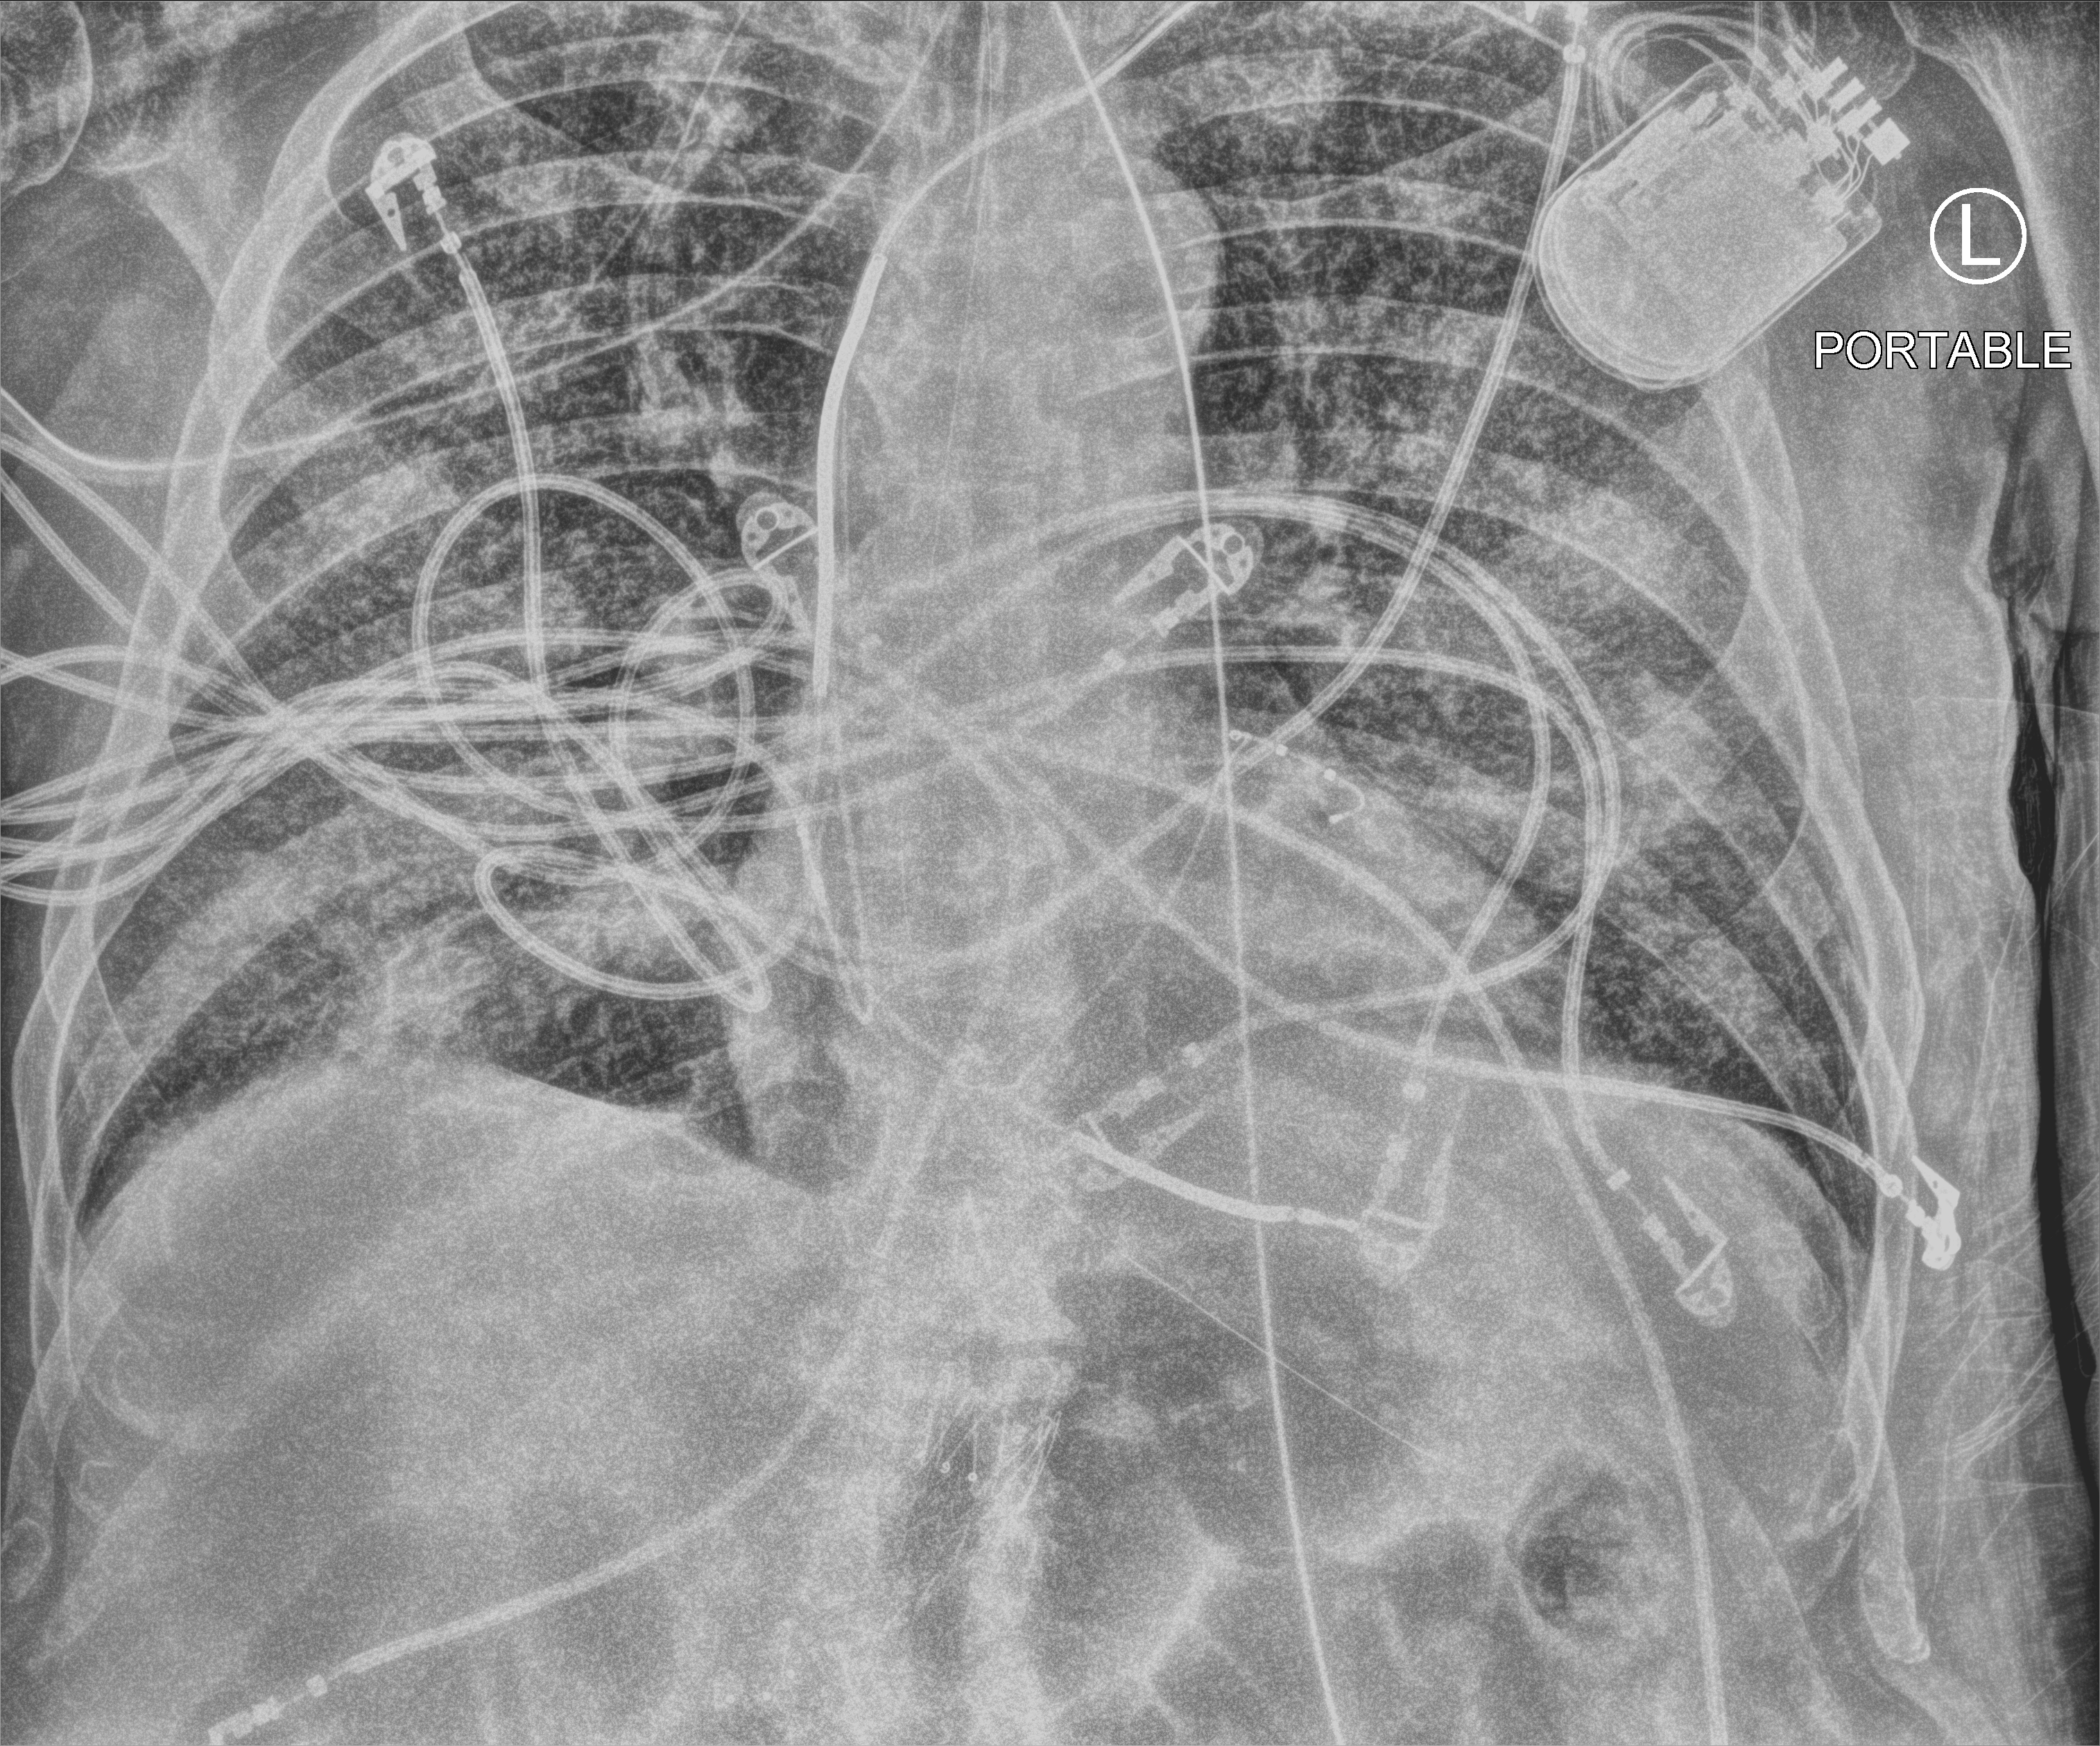
Bedside chest radiograph (computed radiography); anteroposterior (AP) projection. Patient hospitalised with COVID-19; male, aged 60–74 years.
Admission-level facts for this patient (not findings on this image; timing relative to this image not recorded): smoking status (admission record): former; admitted to intensive care during this hospital stay: yes.